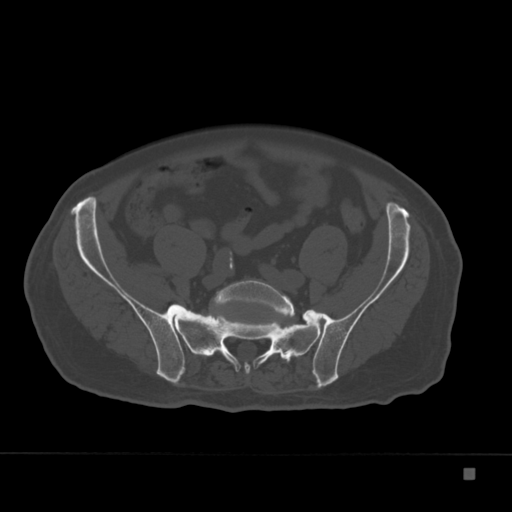
CT including the spine, one axial slice; position 10 of 332 along the scan axis; 120 kVp; bone window (W 1800 / L 400 HU); 1.5 mm slice thickness; 512 × 512 image matrix, field of view 389 × 389 mm. Patient: male, 72 years. Case-level facts recorded for this patient, not image findings: primary cancer: skeletal.
Annotated regions visible in this slice (semi-automatic segmentation, software-assisted and operator-edited):
- L5 vertebra: bounding box [x1, y1, x2, y2] px = [214, 280, 294, 317]